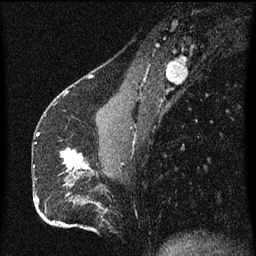
Breast MRI (dynamic contrast-enhanced), one sagittal slice; position 25 of 60 along the scan axis; dynamic contrast-enhanced series, image 2 of 3 at this slice position (ordered by acquisition); 1.5 T; TE 4.2 ms, TR 8 ms; 256 × 256 image matrix, field of view 180 × 180 mm. Female patient, age 51 years.
Outlined on this slice (semi-automatically segmented with operator editing):
- analysis volume of interest (the breast-tissue region the enhancement analysis was run in; not a lesion): bounding box (x1, y1, x2, y2) in pixels: (62, 148, 91, 175)
- tumour enhancement mask (voxels above the 70 % enhancement threshold inside the analysis volume of interest): (62, 150, 89, 173)